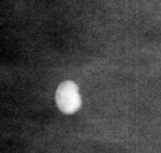
Cropped region of a digitized screen-film mammogram centred on a radiologist-marked abnormality; left breast; CC view; BI-RADS breast density category 4 (scale 1–4).
- Calcifications, morphology round and regular / lucent center / punctate, distribution diffusely scattered; BI-RADS assessment category 2; subtlety rating 5 on a 1 (subtle) to 5 (obvious) scale; benign; no additional work-up was recommended (benign without callback).